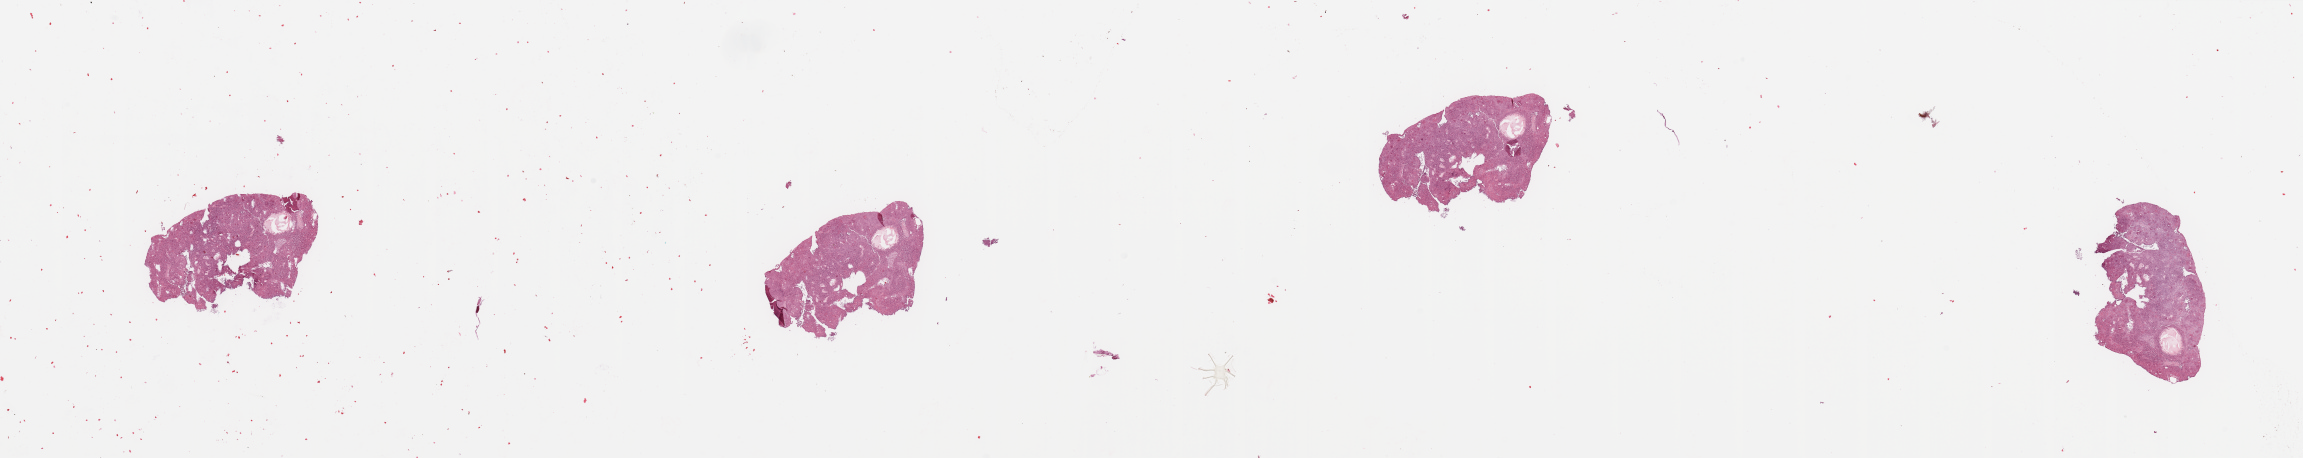
Hematoxylin and eosin (H&E) stained whole-slide image — a low-resolution overview of the entire scanned area, about 36.4 x 7.2 mm (from a 20x scan); tumour tissue sample, sampled site: uterus. Female, 70 y/o. Histologic grade: G3 (poorly differentiated). Pathologist review of this section (percent, as recorded): tumour nuclei 80%, necrosis 2%.
• diagnosis: Endometrioid adenocarcinoma, NOS
• AJCC pathologic stage: I
• primary tumour site (as recorded): fundus